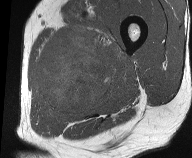
MRI of an extremity soft-tissue mass, one axial slice. Position 22 of 61 along the scan axis. MR volume resampled by the dataset authors to the PET/CT grid (not the native acquisition matrix). 3.27 mm slice thickness. 192 × 158 image matrix. Male patient. Case-level facts recorded for this patient, not image findings: histological type: pleiomorphic liposarcoma; grade: high; site of the primary tumour: left thigh.
Outlined on this slice (expert contour drawn on MRI and transferred to this co-registered scan by the dataset authors):
- gross tumour volume including surrounding oedema: bounding box [x1, y1, x2, y2] px = [34, 25, 129, 118]
- gross tumour volume (mass): [38, 32, 113, 113]